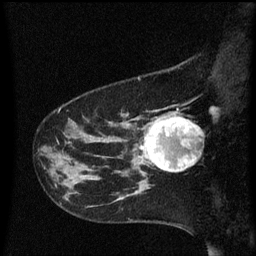
Breast MRI (dynamic contrast-enhanced), one sagittal slice; position 16 of 60 along the scan axis; dynamic contrast-enhanced series, image 2 of 3 at this slice position (ordered by acquisition); 1.5 T; TE 4.2 ms, TR 8.4 ms; 2 mm slice thickness; 256 × 256 image matrix. Patient: female, 41 years. Case-level facts recorded for this patient, not image findings: setting: breast cancer imaged before/during neoadjuvant chemotherapy; receptor status: triple-negative.
Outlined on this slice (semi-automatically segmented with operator editing):
- analysis volume of interest (the breast-tissue region the enhancement analysis was run in; not a lesion): box from (x=138, y=112) to (x=199, y=177) px
- tumour enhancement mask (voxels above the 70 % enhancement threshold inside the analysis volume of interest): (x=141, y=116)–(x=199, y=173)